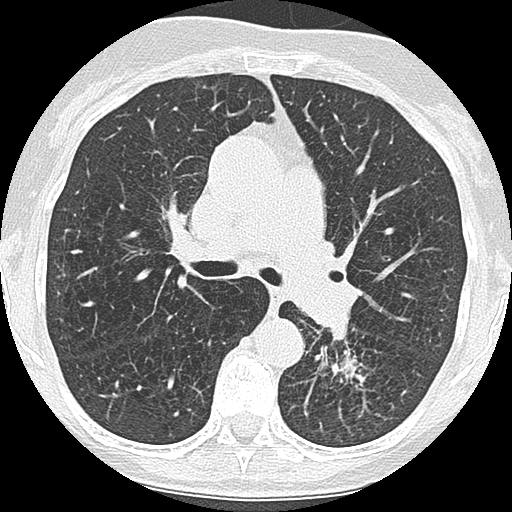
Low-dose screening chest CT, one axial slice. Position 109 of 171 along the scan axis. Lung window (W 1500 / L -600 HU). 2.5 mm slice thickness. 512 × 512 image matrix.
Structures marked on this image (outlined manually by an expert reader):
- lesion 1 (tumor, lower lobe of left lung): bounding box <320,349,365,384> (left, top, right, bottom; pixels)